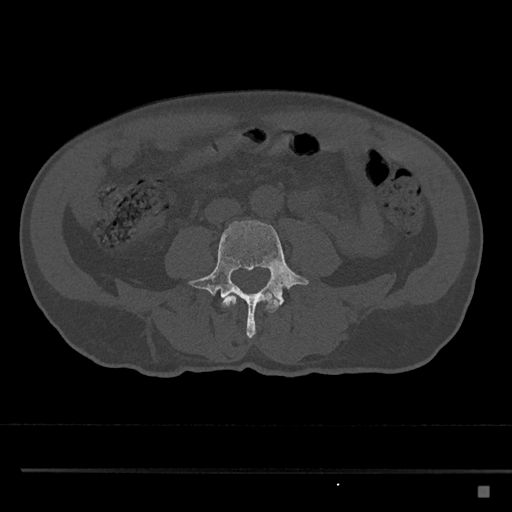
CT including the spine, one axial slice; slice 644 of 797 in the series (ordered by position); reconstruction kernel Br40s/3; bone window (W 1800 / L 400 HU); 512 × 512 image matrix, field of view 391 × 391 mm. Male patient, age 59 years. Case-level facts recorded for this patient, not image findings: primary cancer: prostate.
Annotated regions visible in this slice (semi-automatically segmented with operator editing):
- L3 vertebra: bounding box (x1, y1, x2, y2) in pixels: (222, 291, 278, 313)
- L4 vertebra: (189, 220, 309, 339)